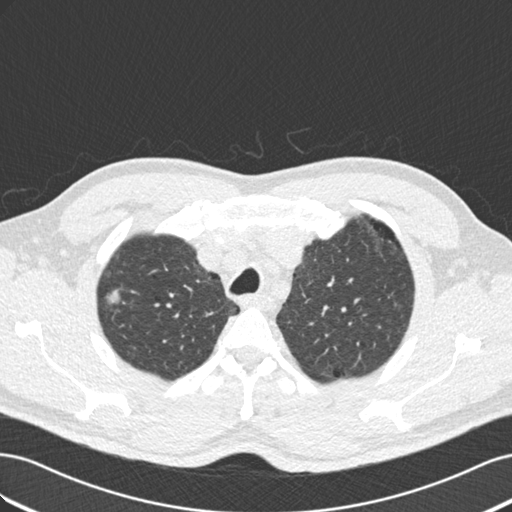
Low-dose screening chest CT, one axial slice; slice 148 of 187 in the series (ordered by position); 120 kVp; lung window (W 1500 / L -600 HU); 512 × 512 image matrix, field of view 360 × 360 mm.
Structures marked on this image (outlined manually by an expert reader):
- lesion 1 (tumor, upper lobe of right lung): bounding box [x1, y1, x2, y2] px = [106, 289, 120, 304]